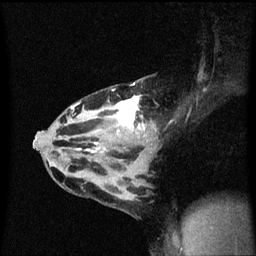
Breast MRI (dynamic contrast-enhanced), one sagittal slice; position 33 of 60 along the scan axis; dynamic contrast-enhanced series, image 2 of 3 at this slice position (ordered by acquisition); 1.5 T; TE 4.2 ms, TR 8.4 ms; 256 × 256 image matrix, field of view 200 × 200 mm. Female patient, age 32 years.
Structures marked on this image (semi-automatic segmentation, software-assisted and operator-edited):
- analysis volume of interest (the breast-tissue region the enhancement analysis was run in; not a lesion): bounding box [x1, y1, x2, y2] px = [55, 80, 160, 167]
- tumour enhancement mask (voxels above the 70 % enhancement threshold inside the analysis volume of interest): [71, 82, 157, 153]